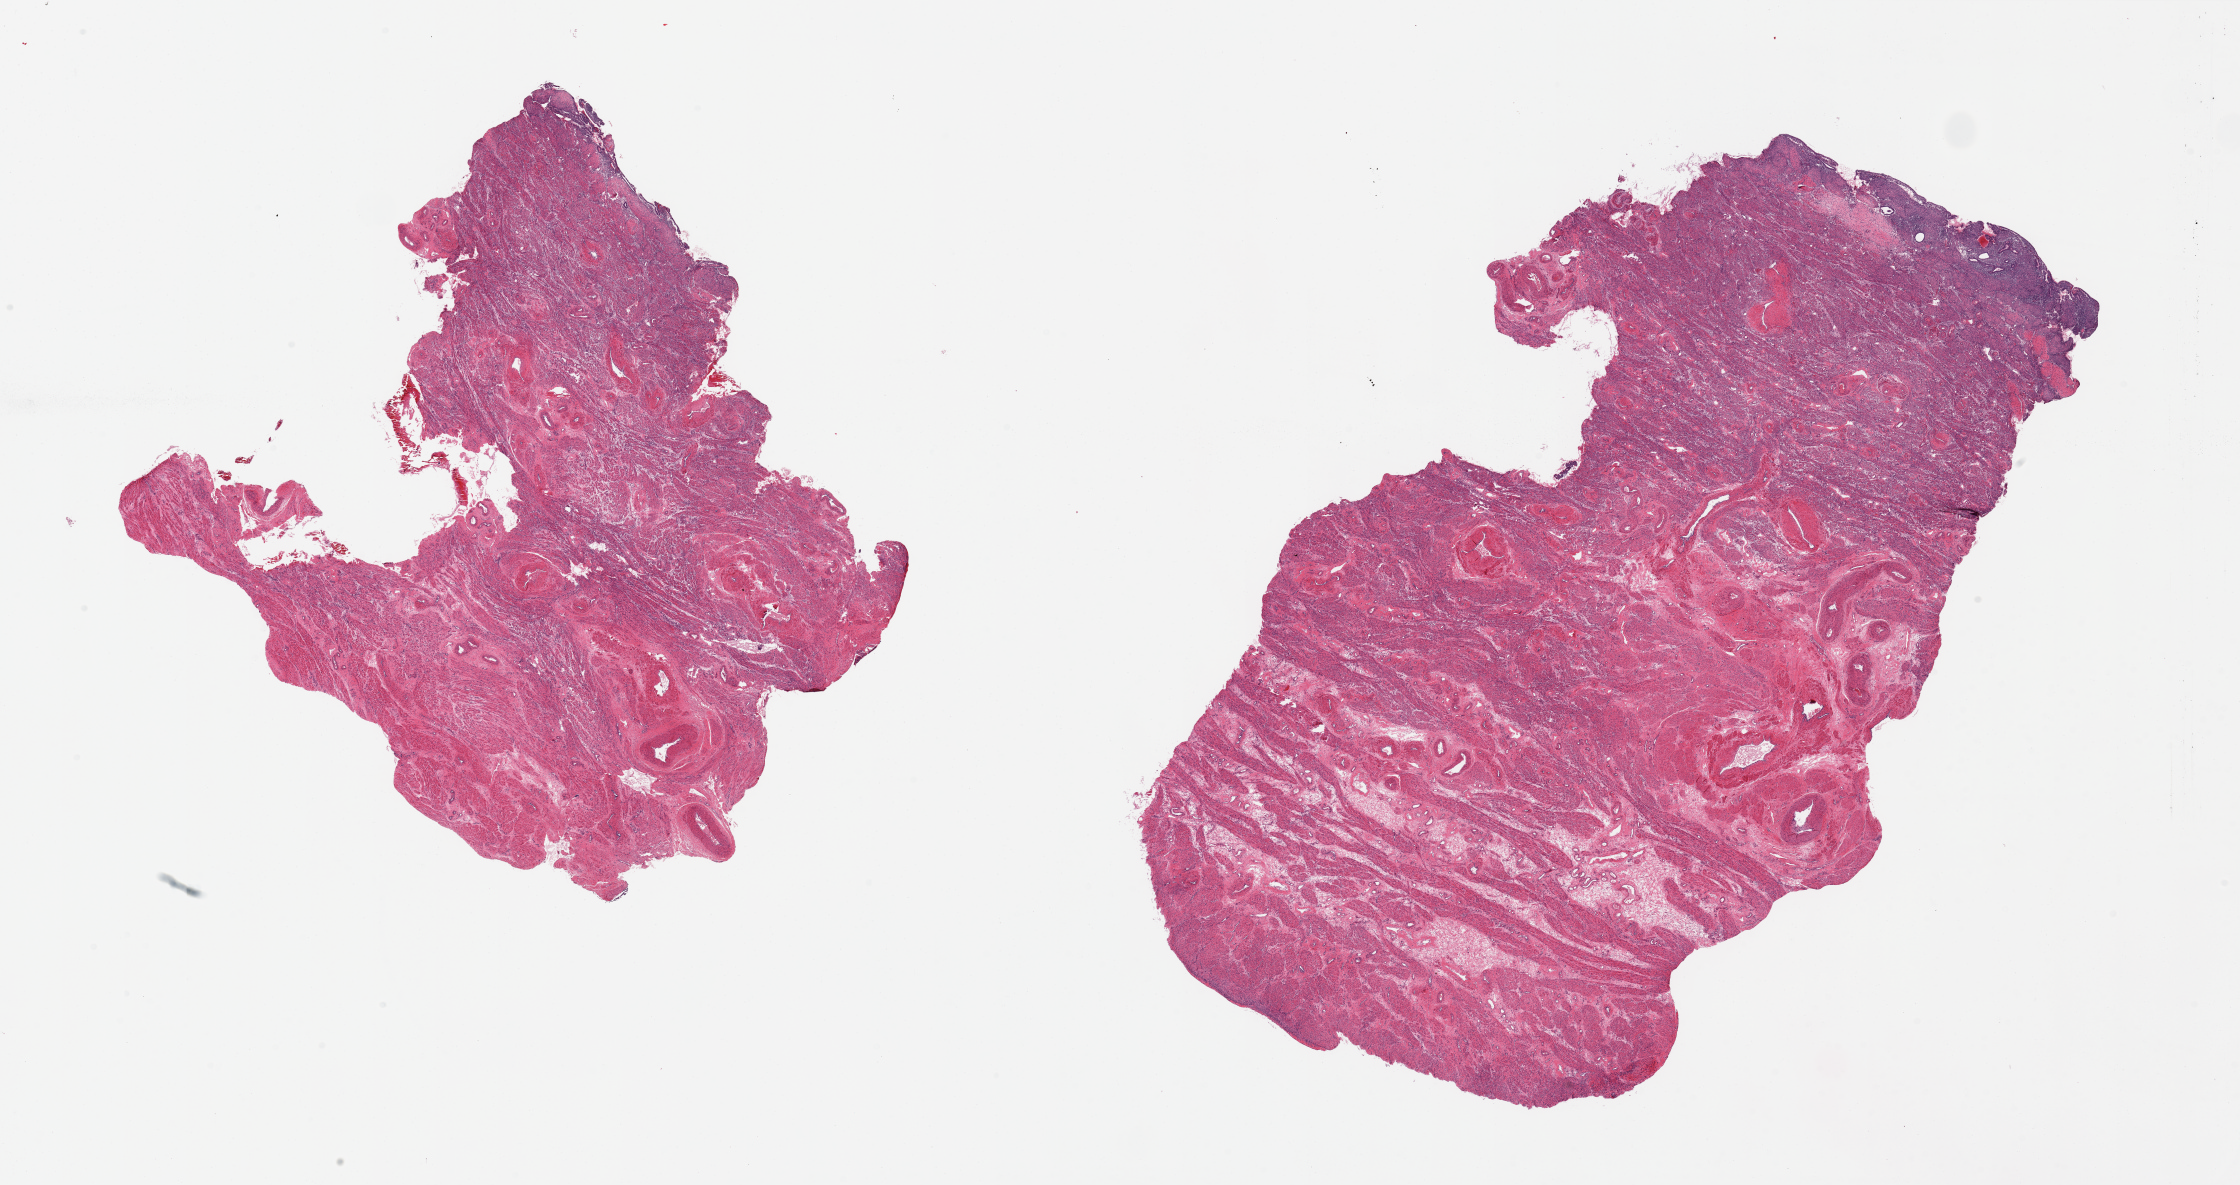
Whole-slide image, haematoxylin and eosin stain, whole scanned area (about 35.4 x 18.7 mm) shown as a low-resolution overview, PAXgene-fixed, paraffin-embedded tissue, section of uterus (target tissue), donor tissue sample. Donor sex: female.
Reviewer comment on this tissue sample: 2 pieces, 11x10 & 16.5x10.5mm; foci of proliferative endometrium ~0.5mm thick.